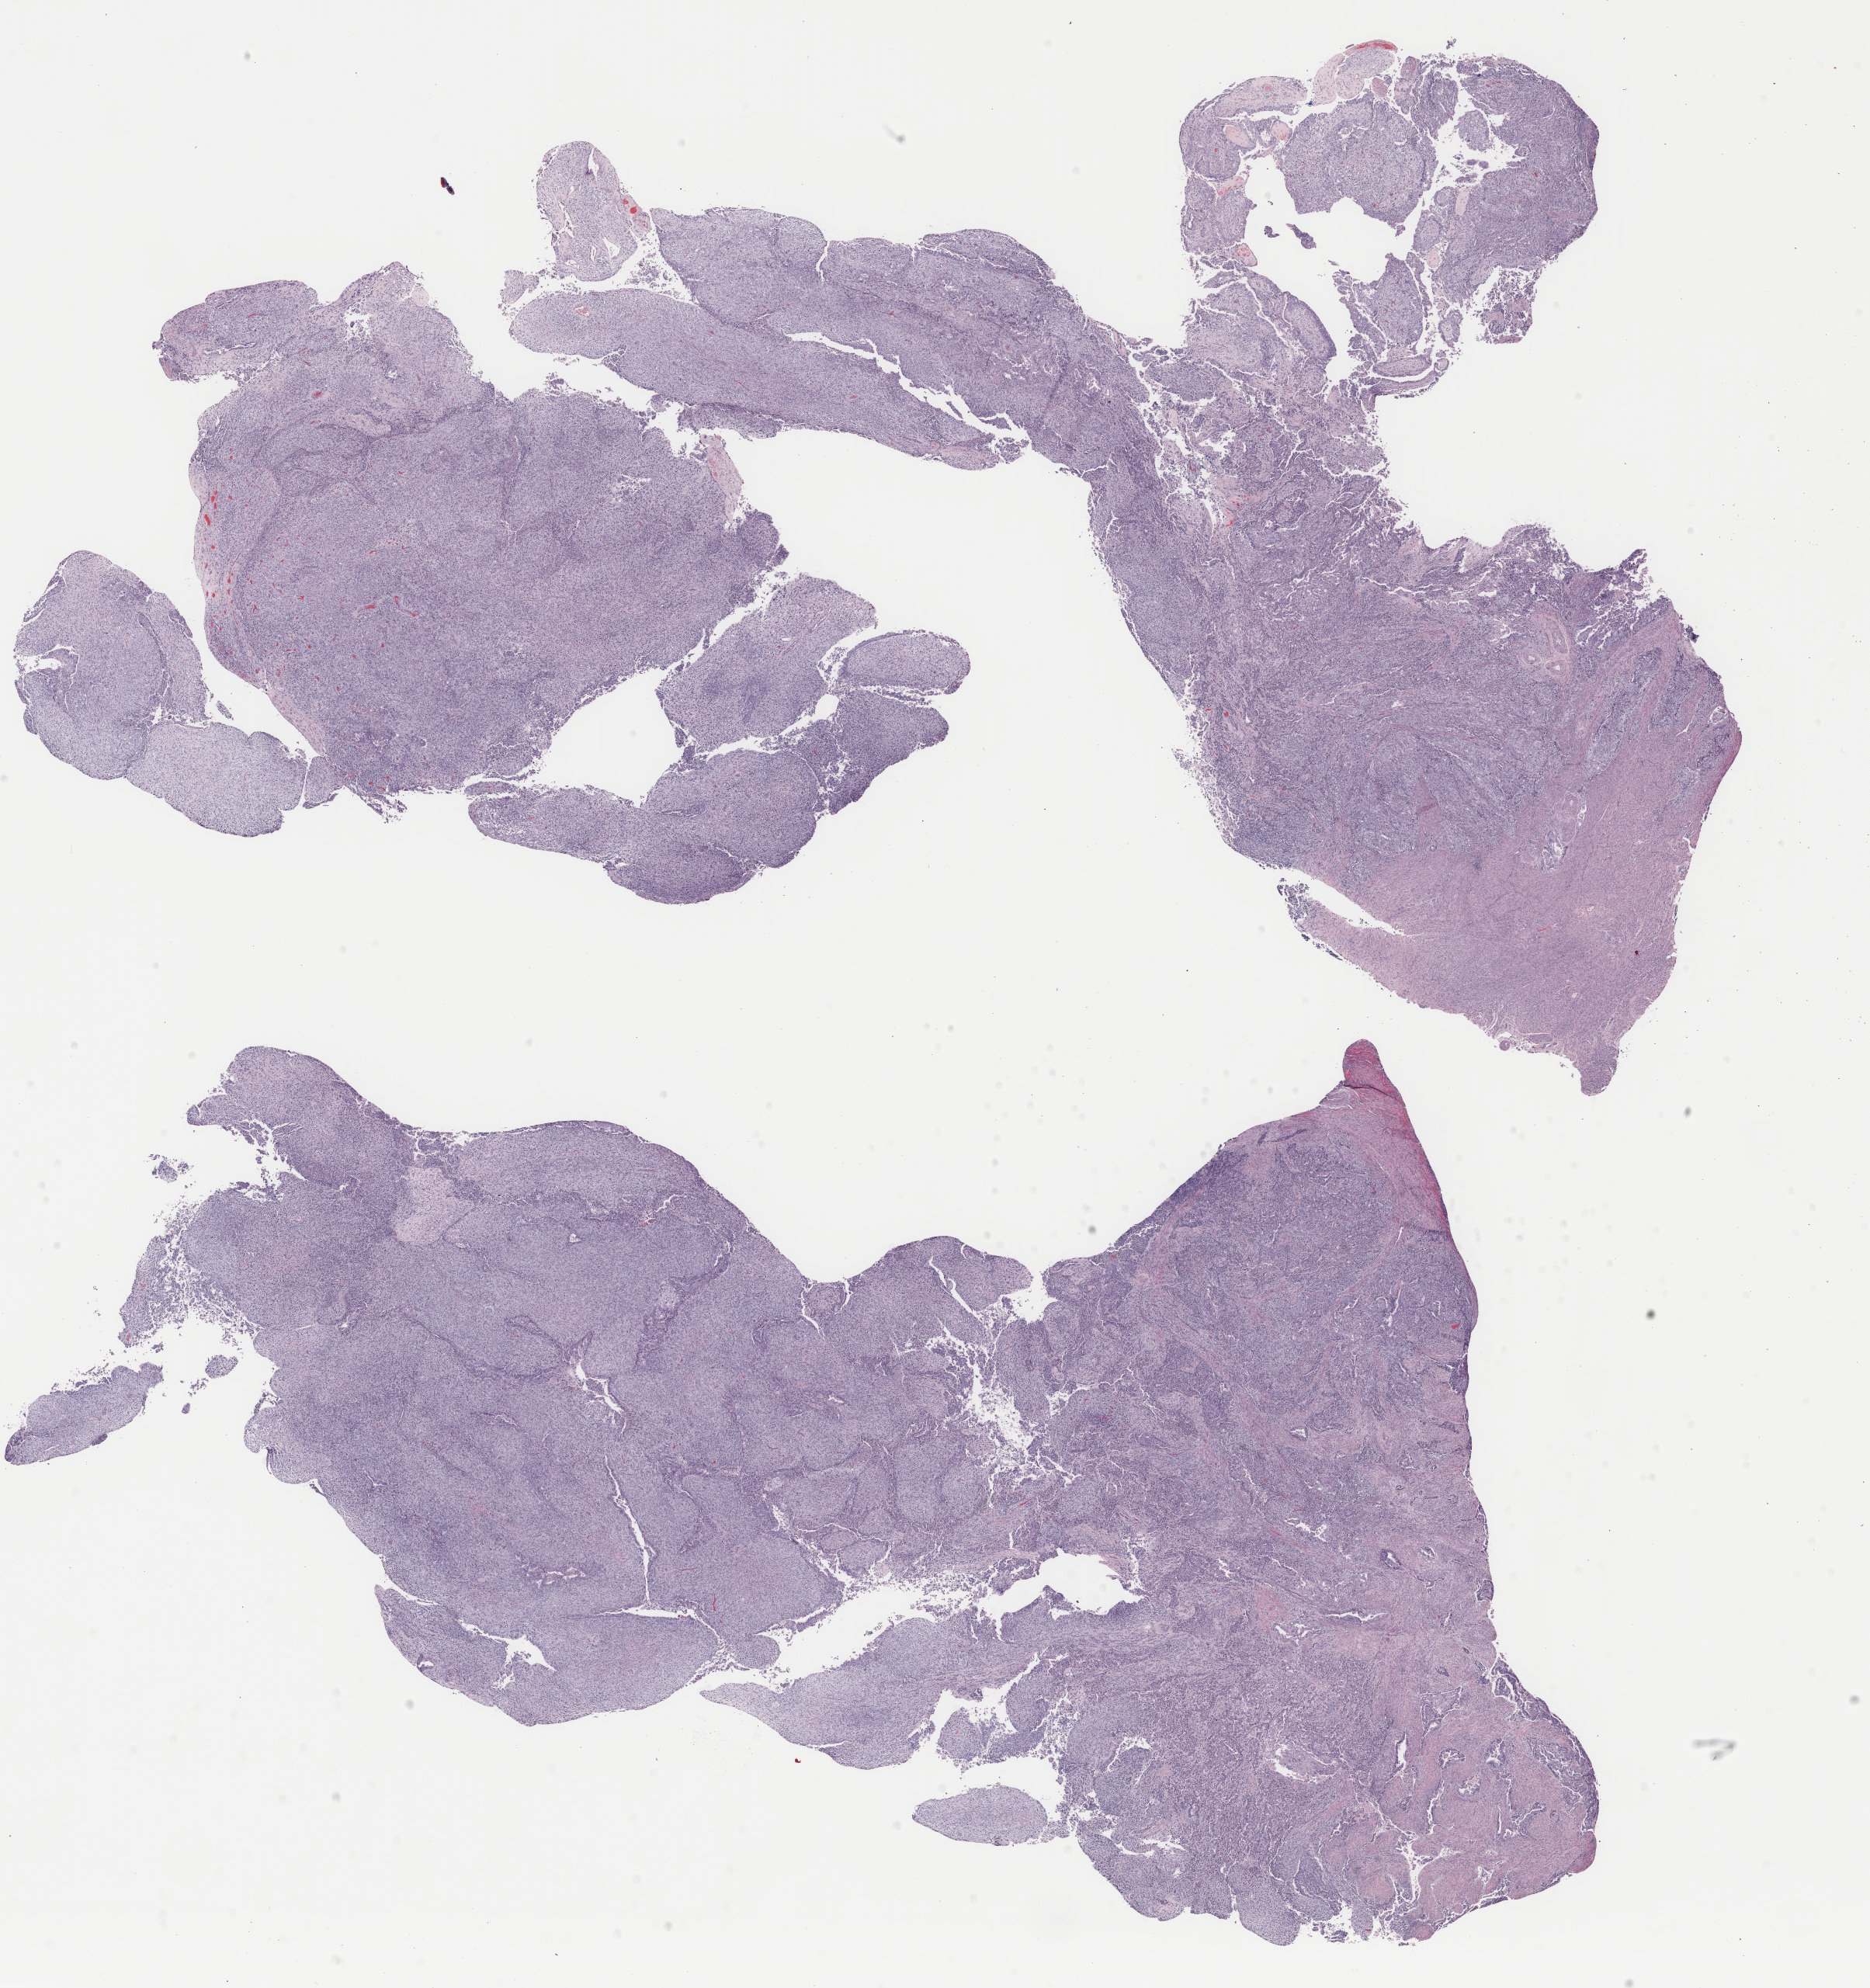
Digitized H&E-stained tissue section (whole slide) — a low-resolution overview of the entire scanned area, about 19.1 x 20.3 mm (from a 40x scan); formalin-fixed paraffin-embedded (FFPE) diagnostic section; uterus, primary tumour sample. Female patient; age at initial diagnosis 69 years.
- pathologic diagnosis: Mullerian mixed tumor (endometrium)
- FIGO stage: IIIC1